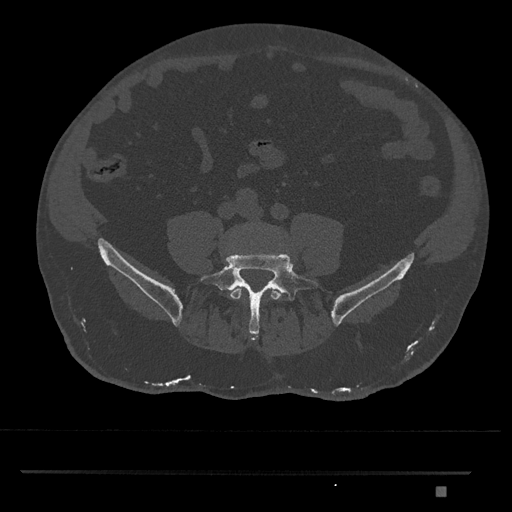
CT including the spine, one axial slice; slice 571 of 1134 in the series (ordered by position); reconstruction kernel Br40s/3; 120 kVp; bone window (W 1800 / L 400 HU); 0.5 mm slice thickness; 512 × 512 image matrix, field of view 429 × 429 mm. Male patient, age 65 years. From the clinical record (not read from this slice): primary cancer: prostate.
Annotated regions visible in this slice (semi-automatic segmentation, software-assisted and operator-edited):
- L4 vertebra: bounding box [x1, y1, x2, y2] px = [229, 287, 283, 300]
- L5 vertebra: [200, 251, 322, 338]